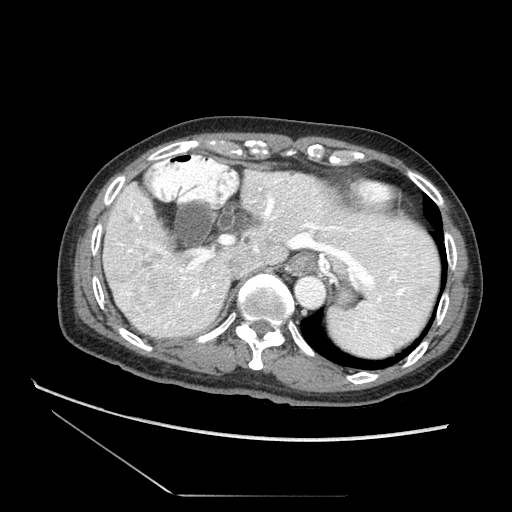
Contrast-enhanced abdominal CT (liver protocol), one axial slice. Slice 58 of 73 in the series (ordered by position). Reconstruction kernel STANDARD. Soft-tissue window (W 400 / L 40 HU). 2.5 mm slice thickness. 512 × 512 image matrix. Case-level facts recorded for this patient, not image findings: diagnosis: hepatocellular carcinoma (patient treated with transarterial chemoembolisation; whether this scan precedes or follows treatment is not stated here); TNM stage (as recorded): Stage-II; Child-Pugh class: A; tumour differentiation: moderately differentiated; tumour nodularity: multinodular.
Outlined on this slice (semi-automatic segmentation, software-assisted and operator-edited):
- liver parenchyma outside the tumour (the mass and vessels are separate outlines, so this box may not span the whole liver): bounding box [x1, y1, x2, y2] px = [103, 171, 444, 350]
- mass: [116, 260, 184, 321]
- liver vessels: [136, 187, 404, 288]